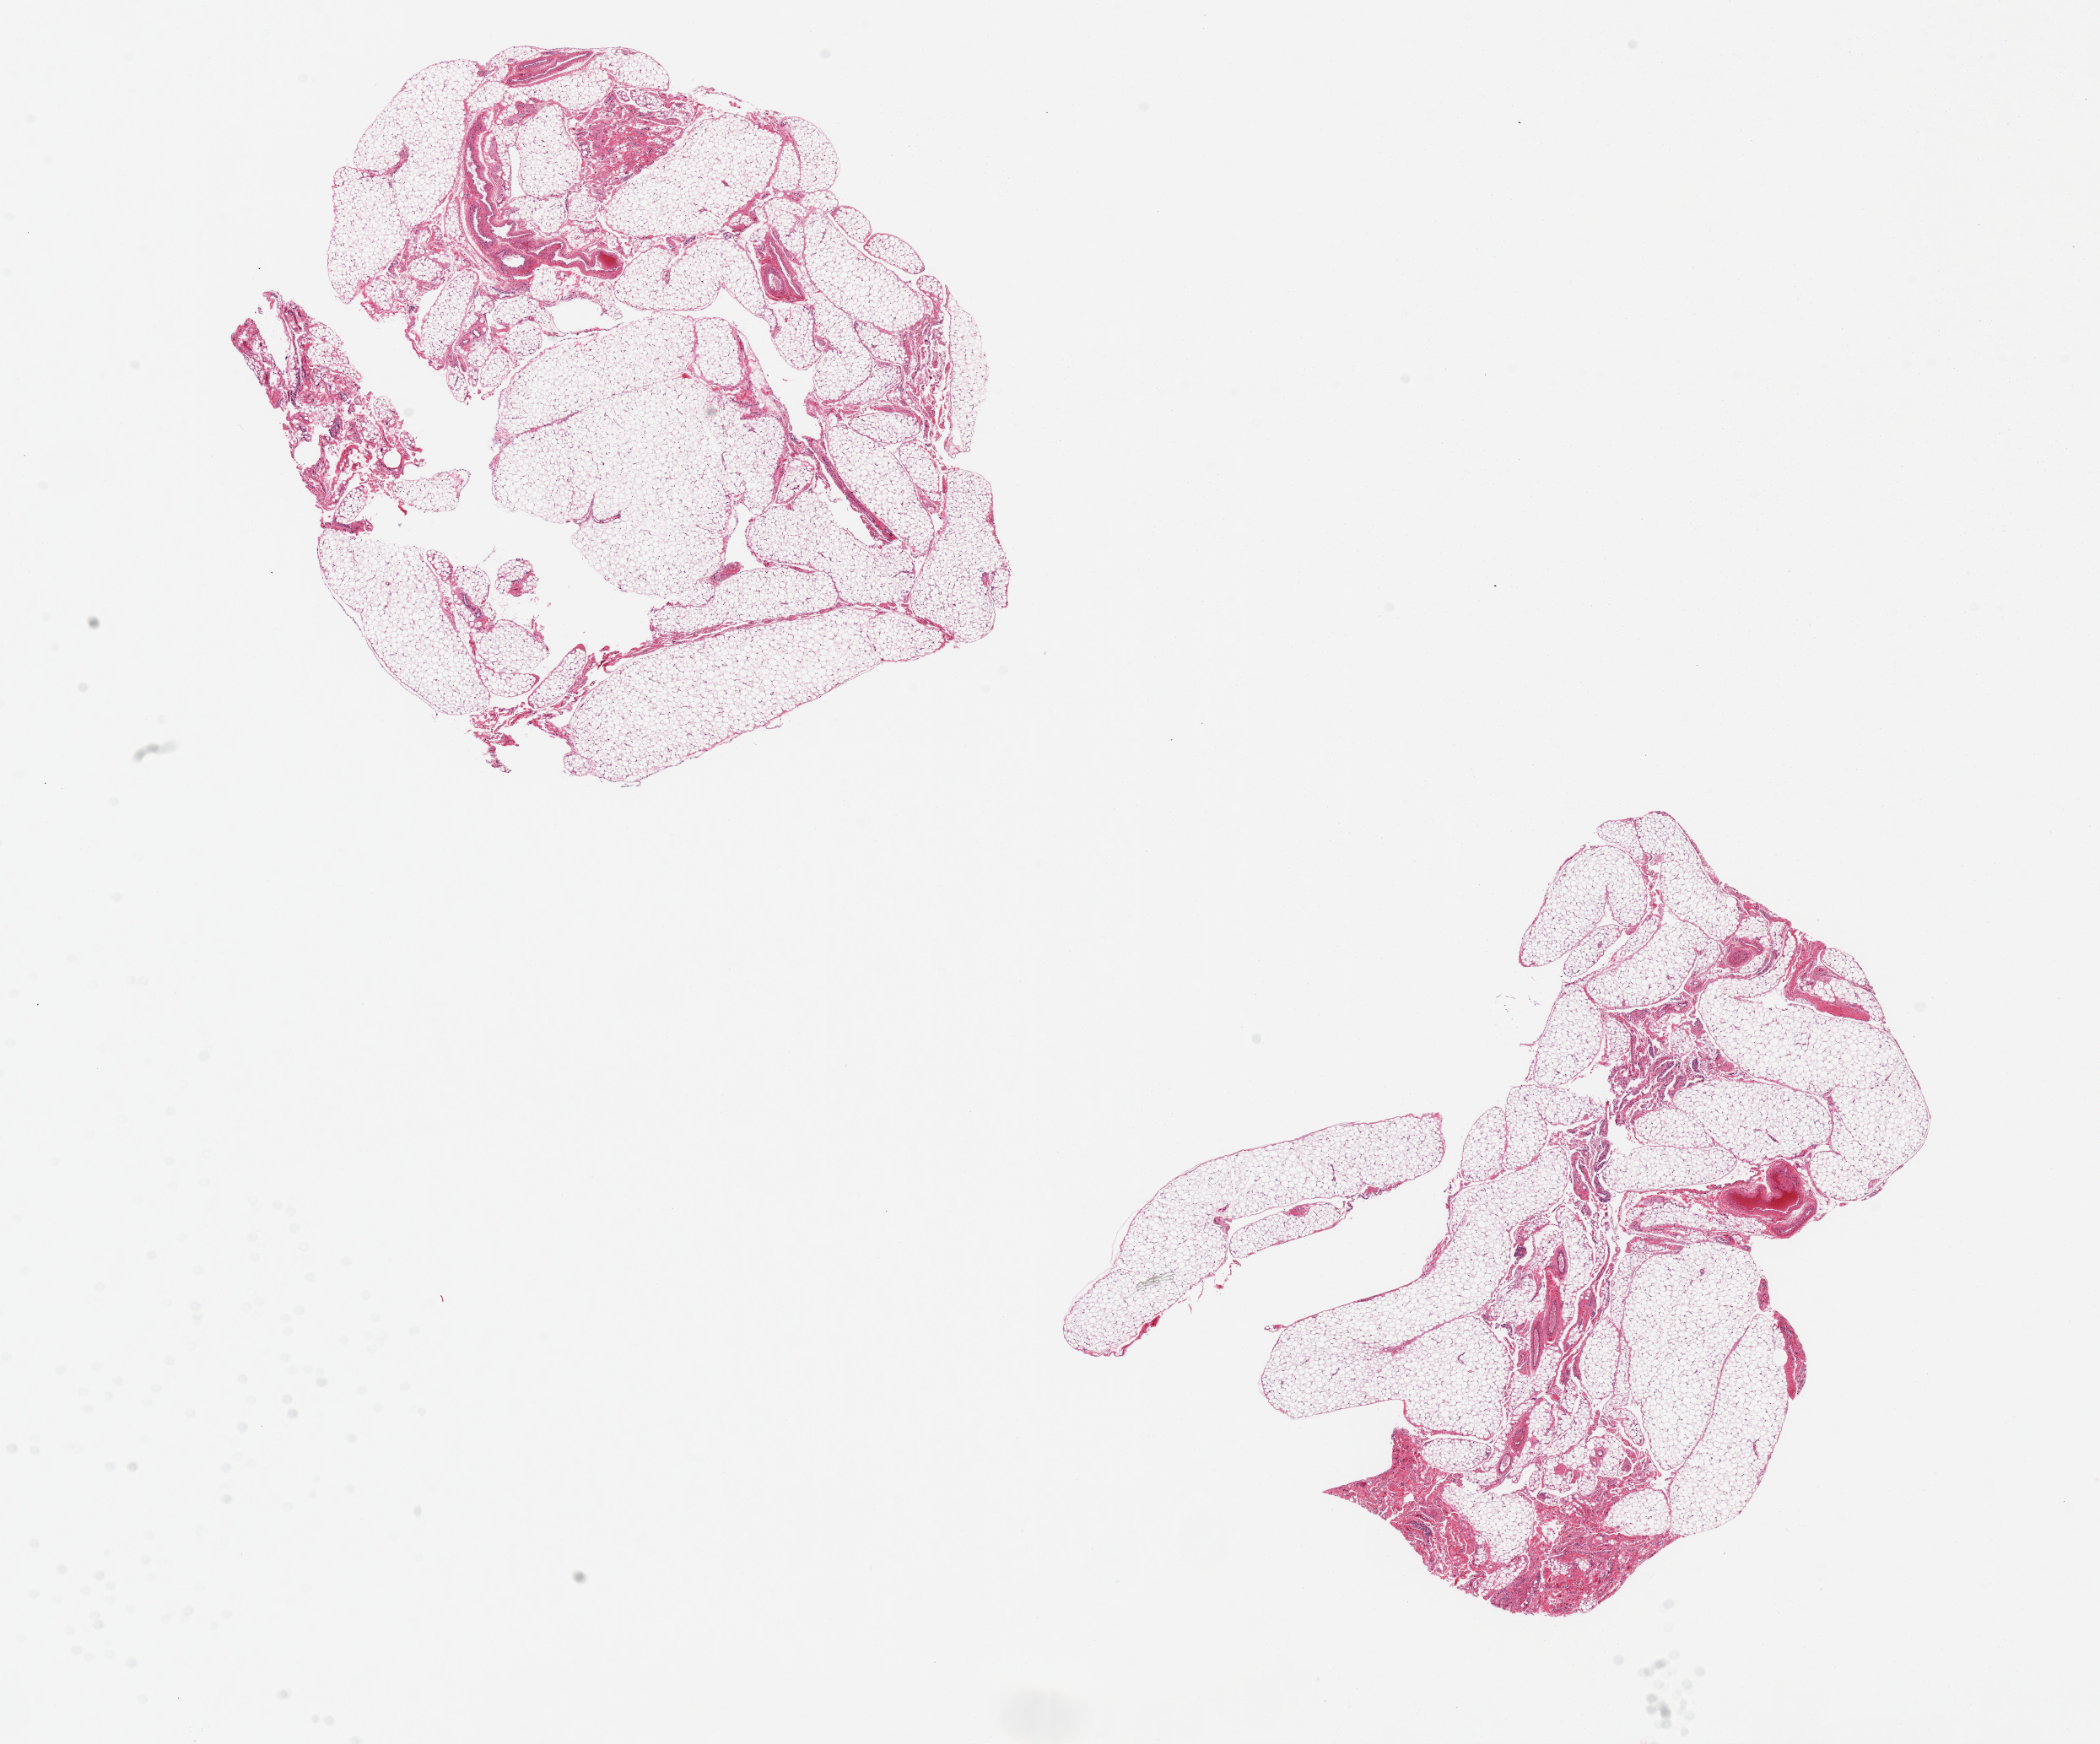
Haematoxylin and eosin whole-slide image, low-resolution overview of the scanned area, about 19.7 x 16.4 mm (acquisition: 20x scan), PAXgene-fixed, paraffin-embedded tissue, sampled site (target tissue): omentum, tissue donor sample.
* reviewer comment on this tissue sample: 2 pieces ~7x5mm